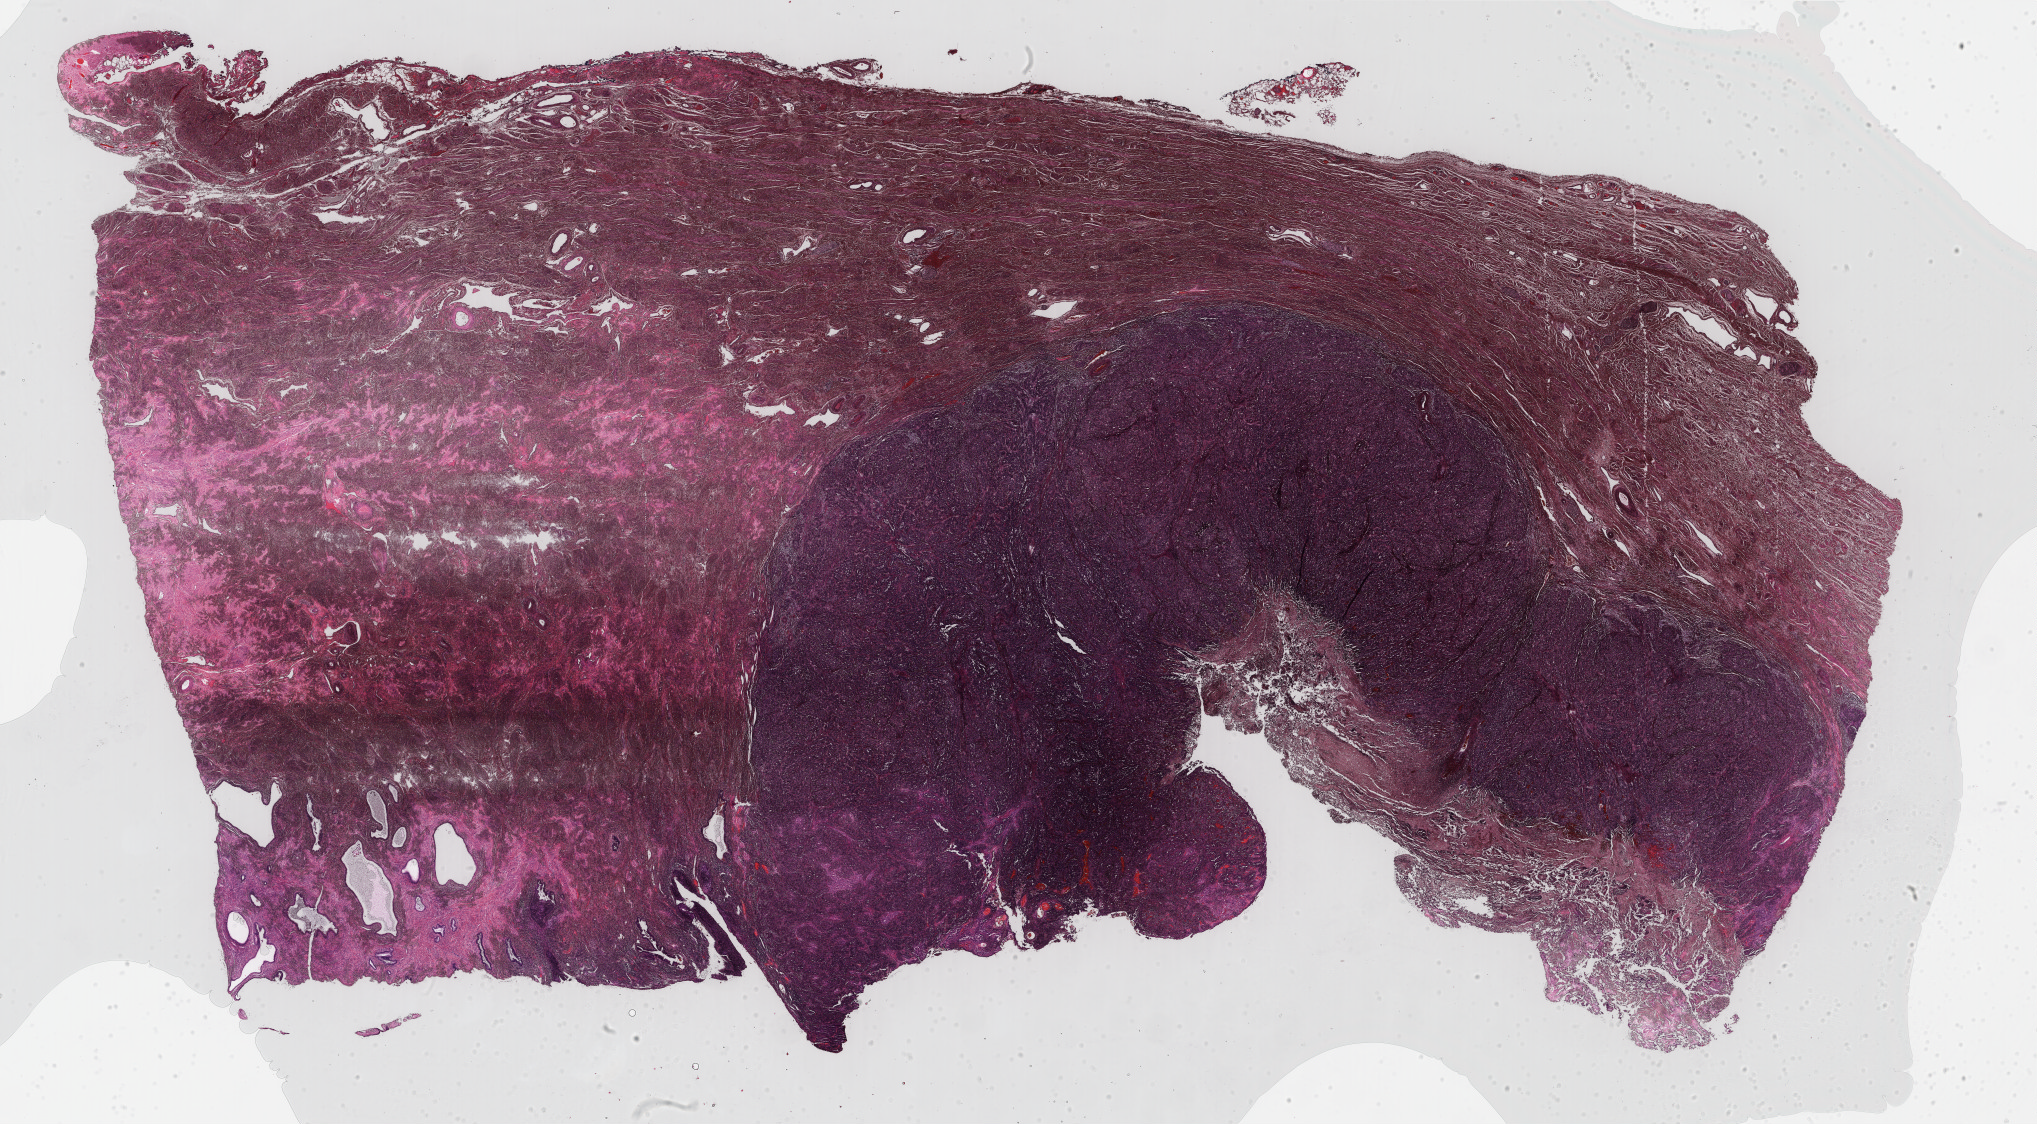
Whole-slide histology image, Hematoxylin and eosin (H&E) stained, whole scanned area (about 32.3 x 17.8 mm, acquisition: 40x scan) shown as a low-resolution overview, FFPE section, primary tumour sample from the cervix. Patient: female, age at initial diagnosis 51 years. Histologic grade: G3 (poorly differentiated).
Diagnosis: Squamous cell carcinoma, NOS.